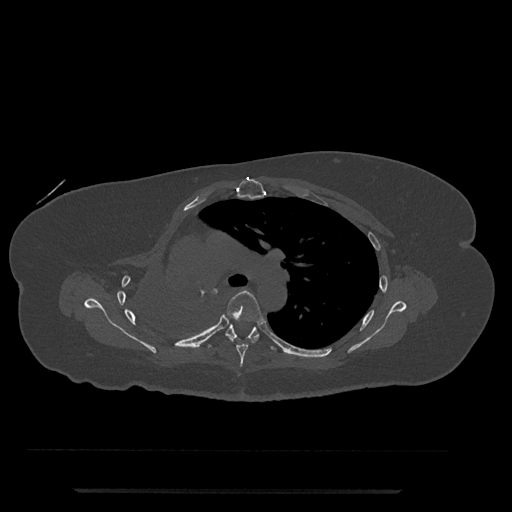
CT including the spine, one axial slice; slice 522 of 797 in the series (ordered by position); reconstruction kernel Br40s/3; 120 kVp; bone window (W 1800 / L 400 HU); 512 × 512 image matrix. Patient: female, 51 years. From the clinical record (not read from this slice): primary cancer: neuro; vertebrae with lytic lesions (as recorded): T8.
Outlined on this slice (semi-automatic segmentation, software-assisted and operator-edited):
- T5 vertebra: box from (x=225, y=290) to (x=264, y=367) px
- T6 vertebra: (x=208, y=324)–(x=276, y=351)